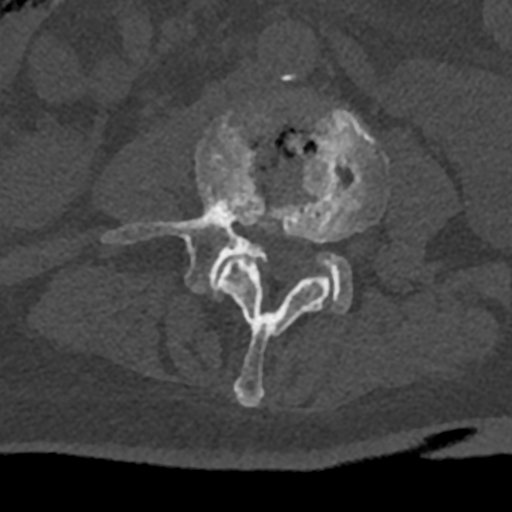
CT including the spine, one axial slice; position 290 of 797 along the scan axis; reconstruction kernel Br40s/3; bone window (W 1800 / L 400 HU); 0.5 mm slice thickness; 512 × 512 image matrix. Male patient, age 74 years. Case-level facts recorded for this patient, not image findings: primary cancer: renal; vertebrae with lytic lesions (as recorded): T10, L1, L2, L3, L4, L5.
Structures marked on this image (semi-automatically segmented with operator editing):
- L3 vertebra: bounding box (x1, y1, x2, y2) in pixels: (218, 107, 388, 407)
- L4 vertebra: (103, 114, 352, 313)